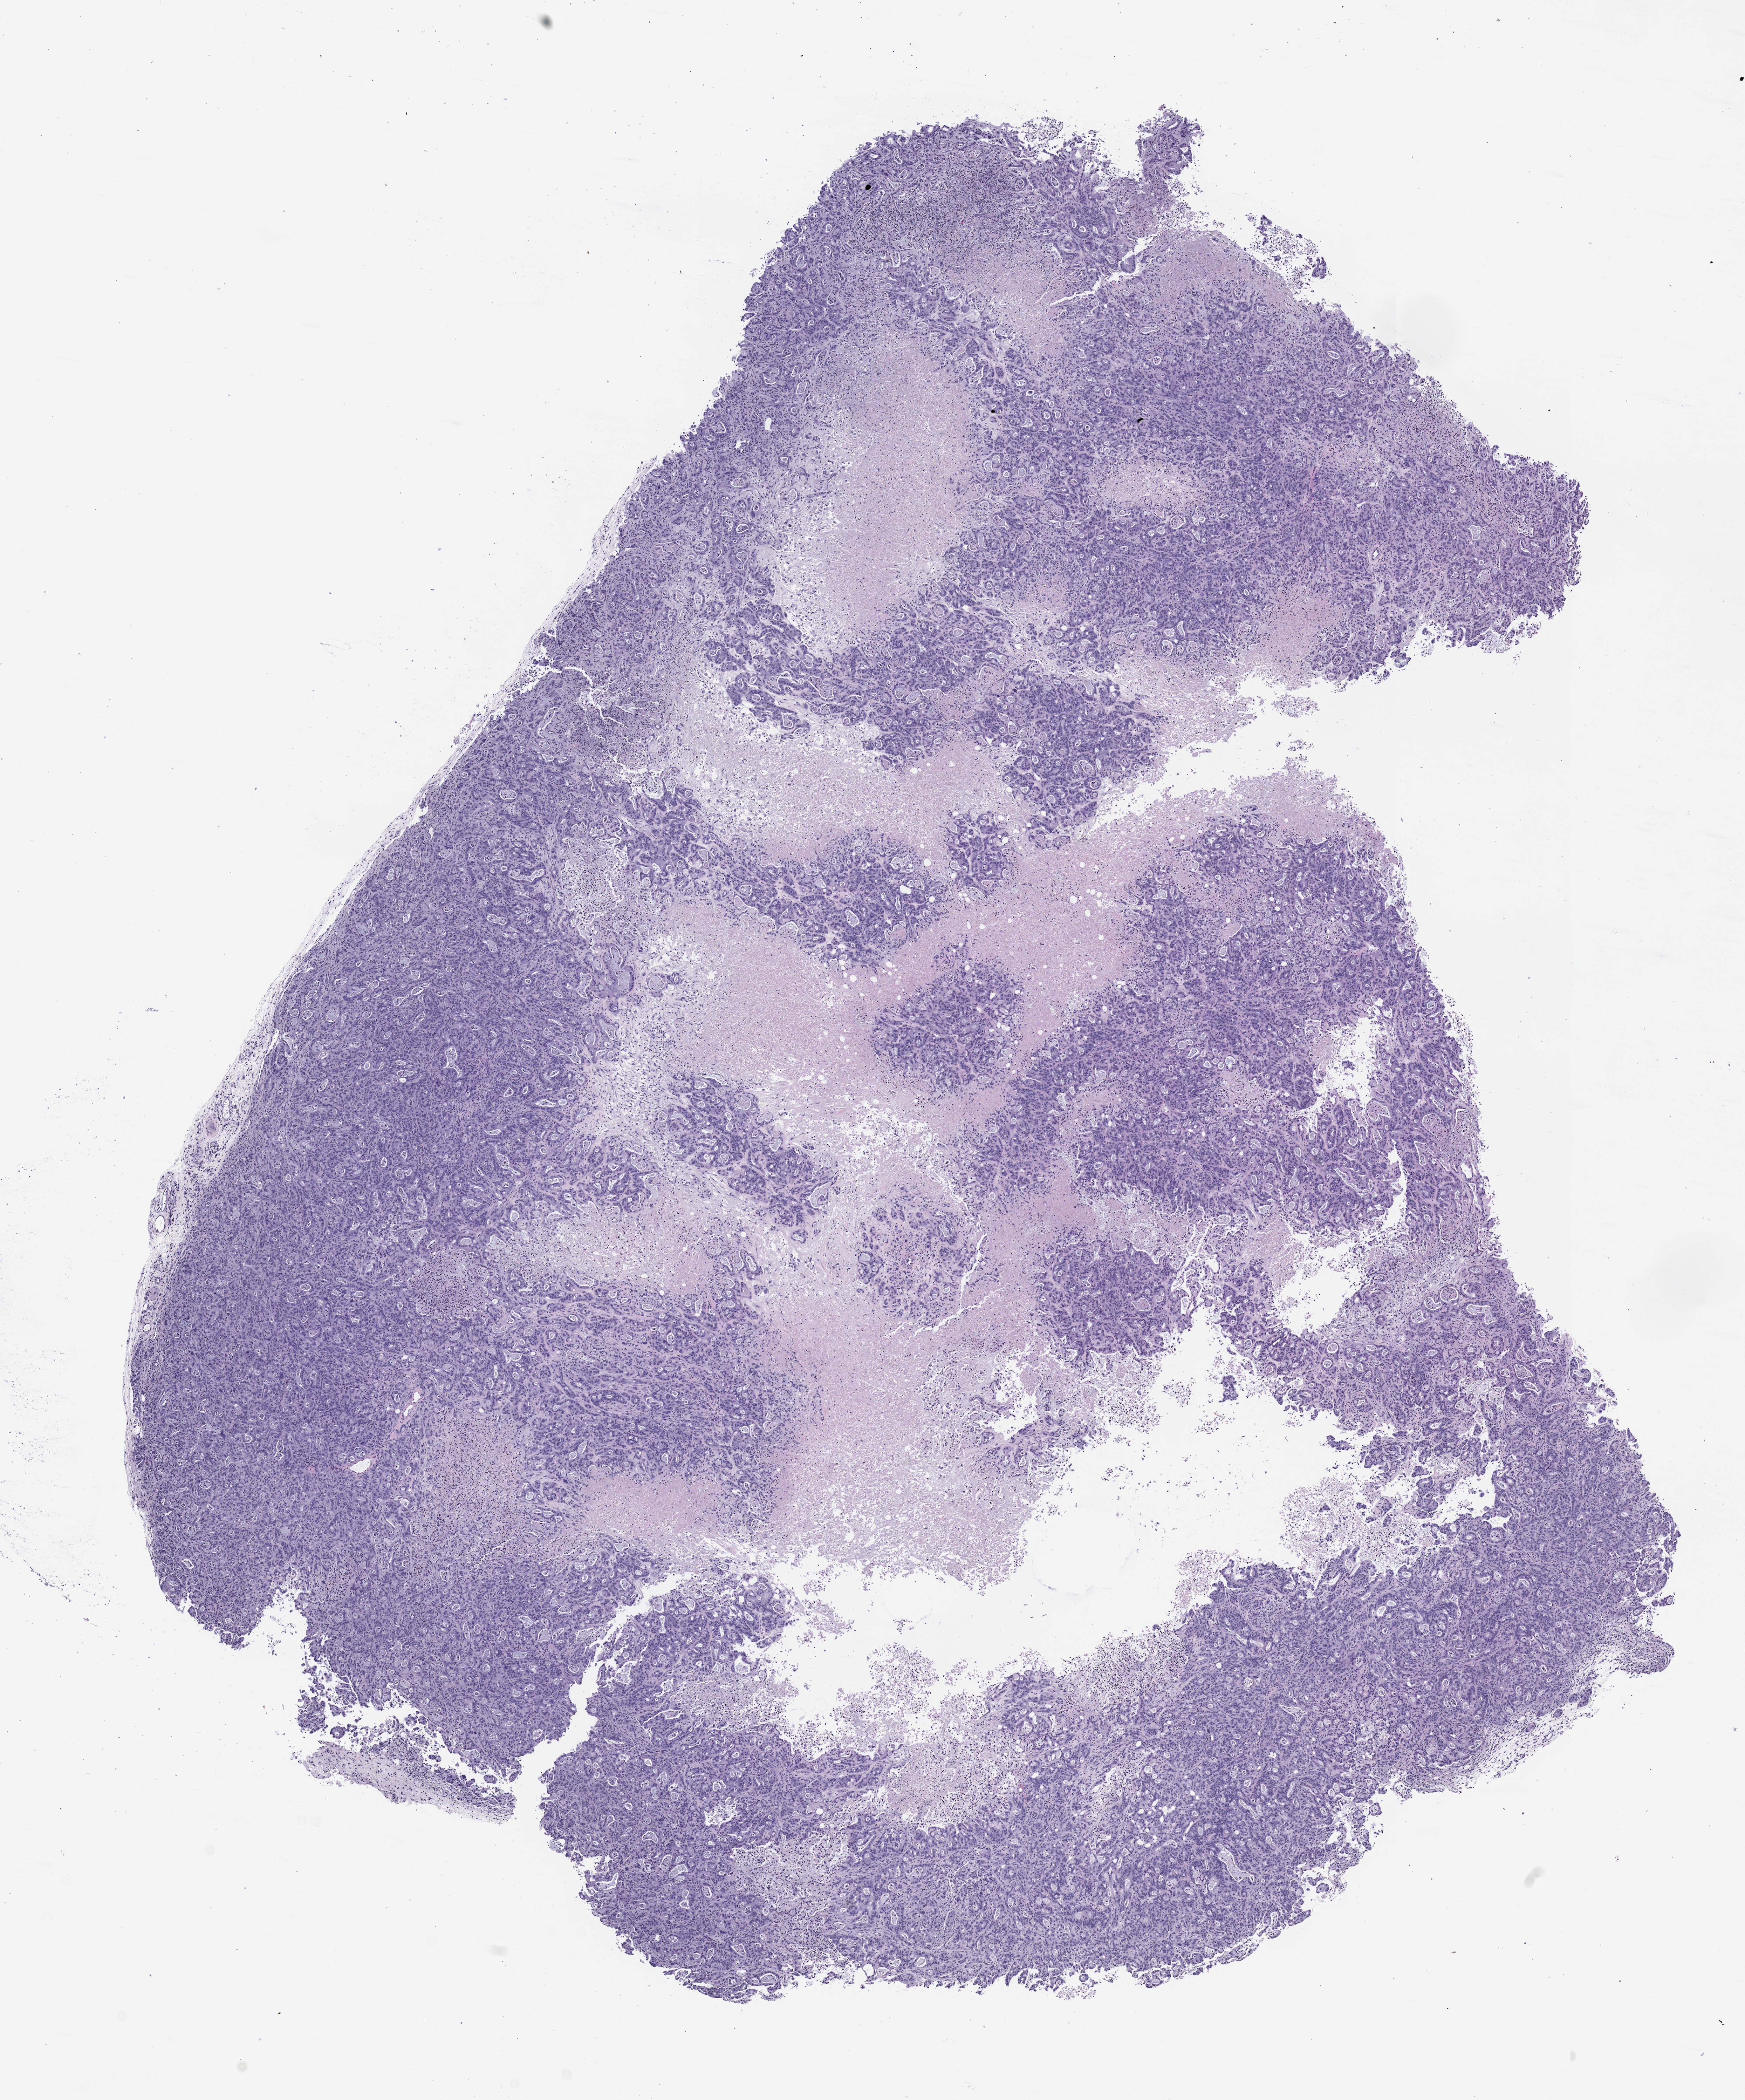
Haematoxylin and eosin whole-slide image of a patient-derived xenograft (PDX) tumor grown in a mouse — a low-resolution overview of the entire scanned area, about 10.0 x 12.0 mm; formalin-fixed paraffin-embedded section; originating tumor site category: pancreas.
Originating patient diagnosis: Pancreatic Adenocarcinoma.